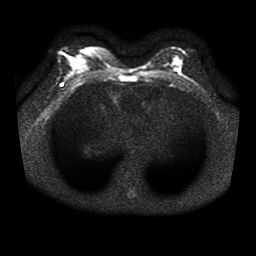
Breast MRI, one axial slice. Position 19 of 41 along the scan axis. Diffusion-weighted series; image 2 of 4 stored at this slice position (different b-values; order by instance number). 1.5 T. 5 mm slice thickness. 256 × 256 image matrix, field of view 330 × 330 mm. Female patient.
Annotated regions visible in this slice (expert manual segmentation):
- tumour on diffusion-weighted imaging: bounding box (x1, y1, x2, y2) in pixels: (174, 59, 181, 66)